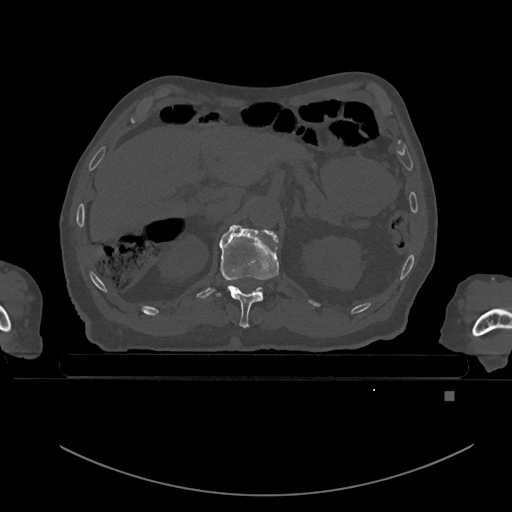
CT including the spine, one axial slice; position 12 of 969 along the scan axis; bone window (W 1800 / L 400 HU); 0.5 mm slice thickness; 512 × 512 image matrix, field of view 456 × 456 mm. Patient: male, 82 years. From the clinical record (not read from this slice): primary cancer: prostate; vertebrae with lytic lesions (as recorded): T11, T9, T8, T2.
Outlined on this slice (semi-automatically segmented with operator editing):
- T11 vertebra: bounding box (x1, y1, x2, y2) in pixels: (216, 227, 279, 328)